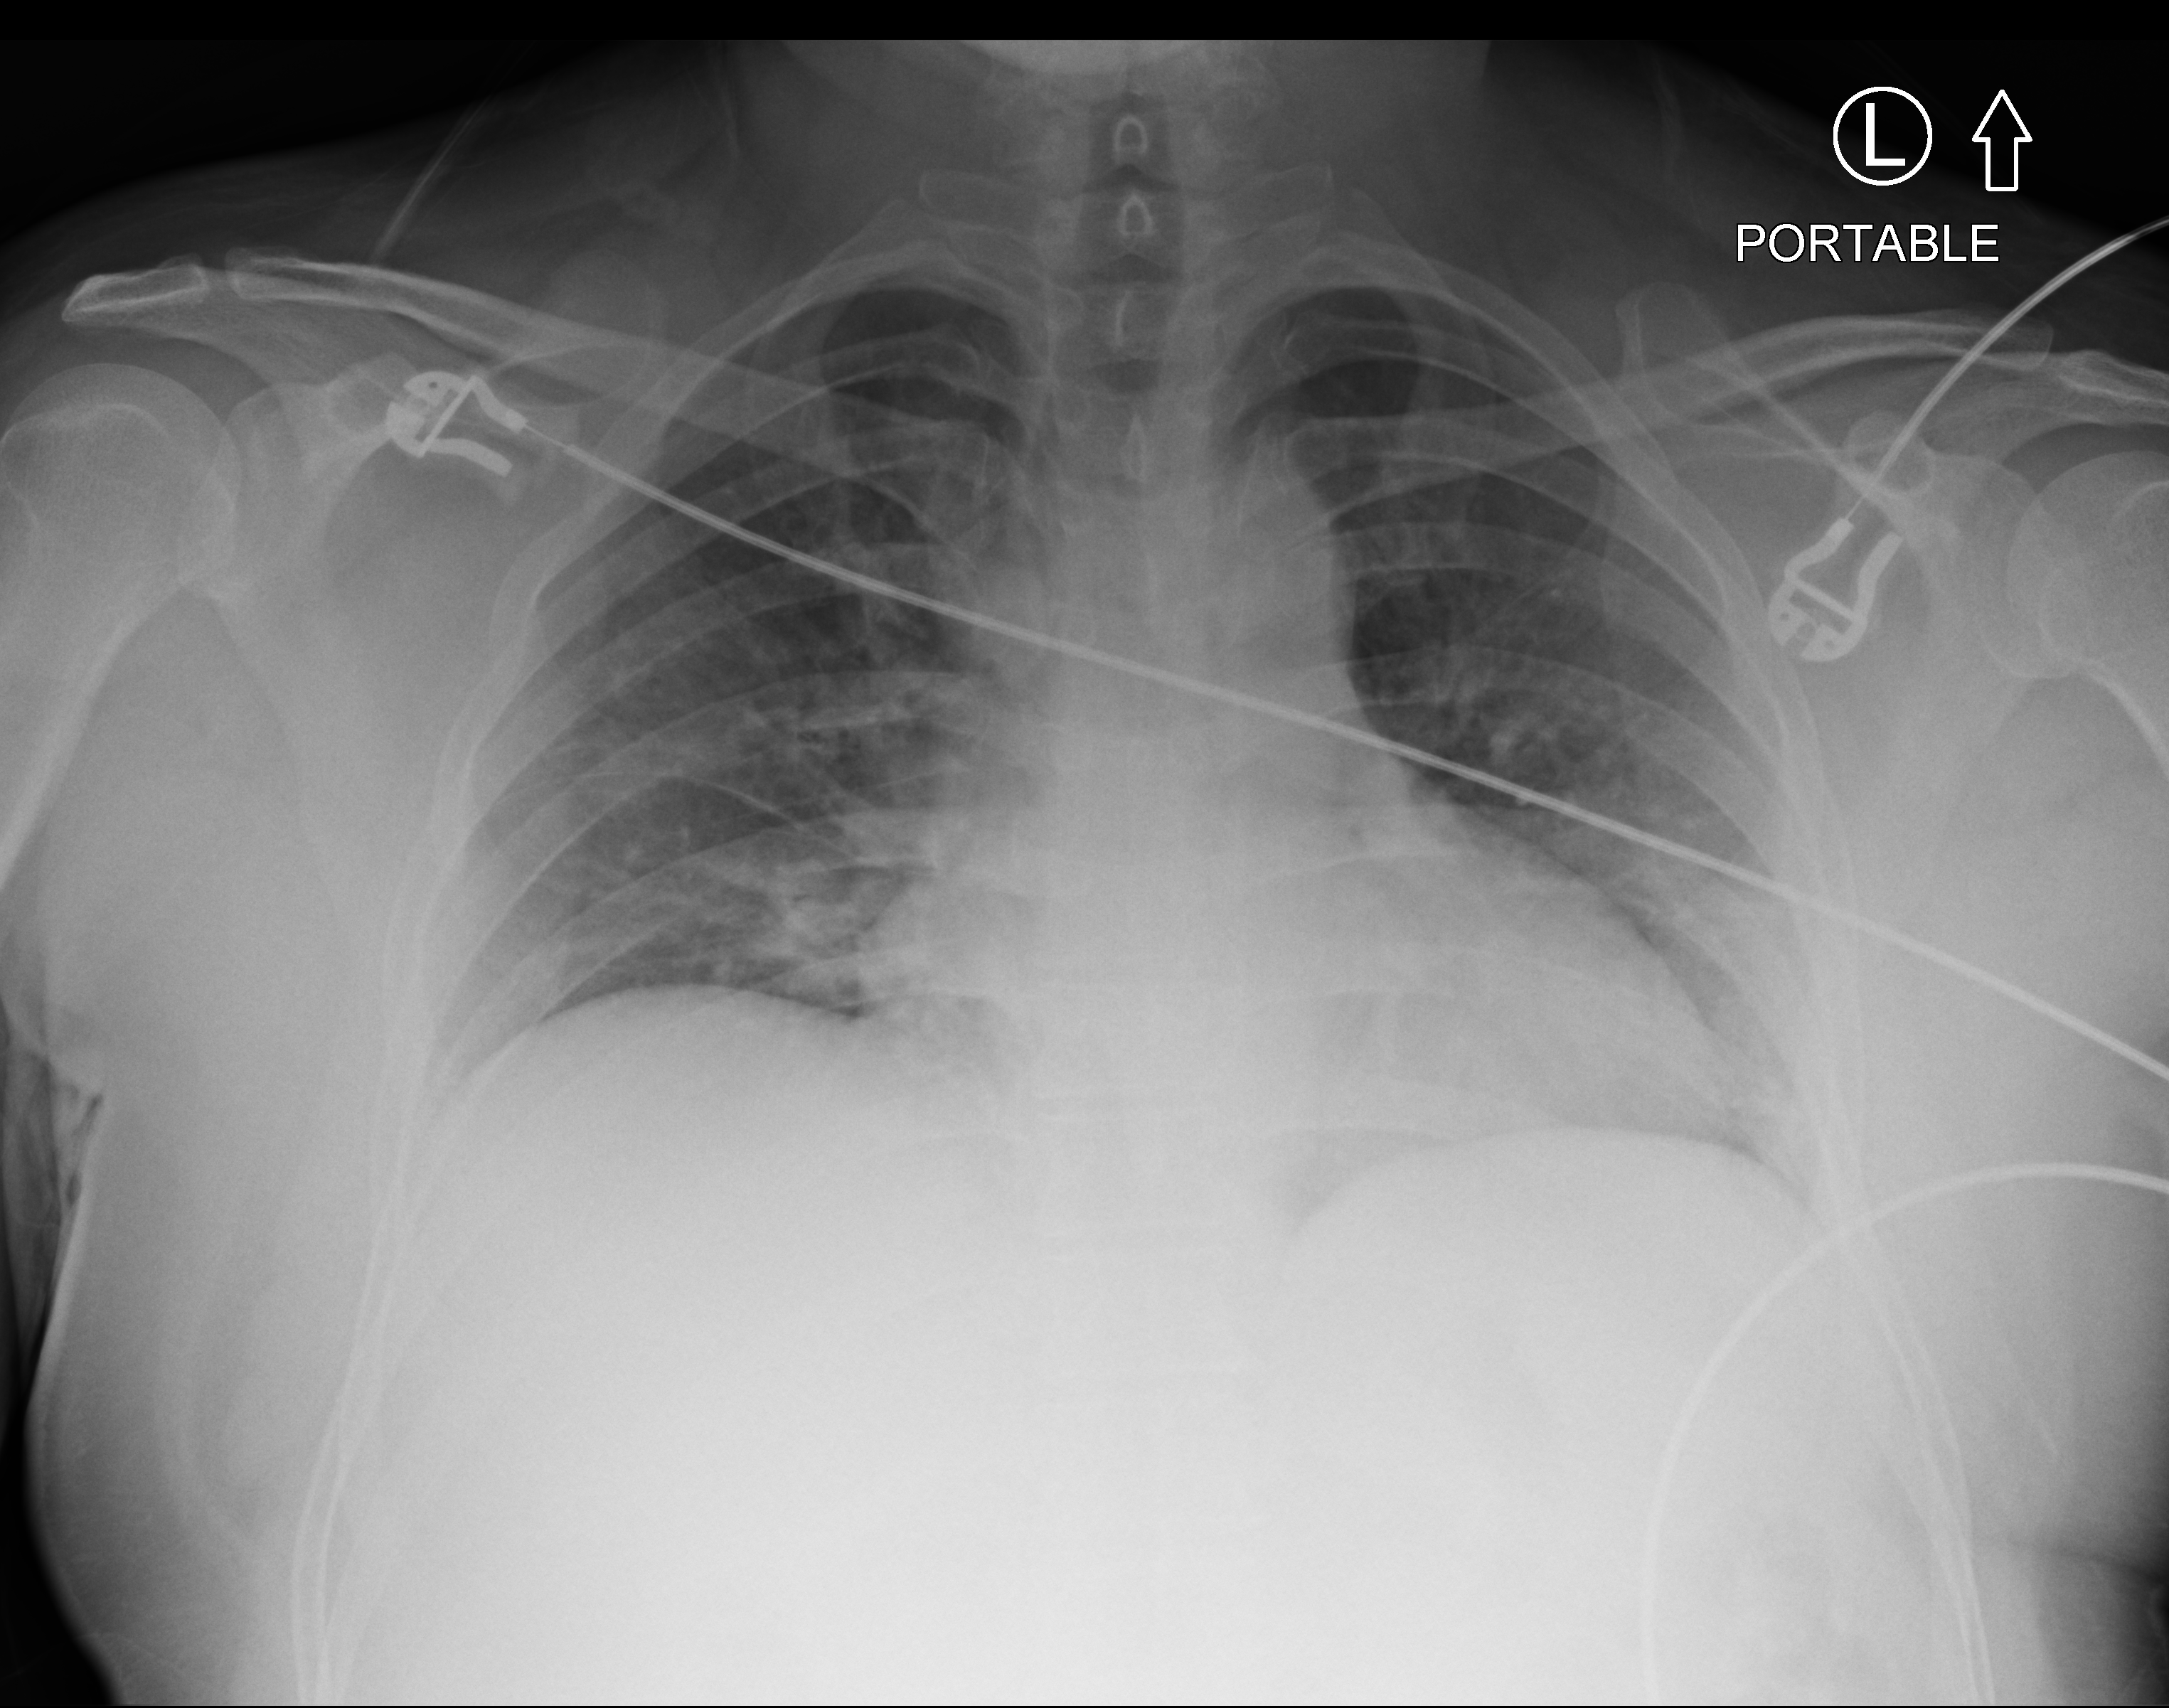
Chest X-ray (portable). Male patient hospitalised with COVID-19, age 18–59 years.
Admission-level facts for this patient (not findings on this image; timing relative to this image not recorded): admitted to intensive care during this hospital stay: no; length of hospital stay: 1 day.